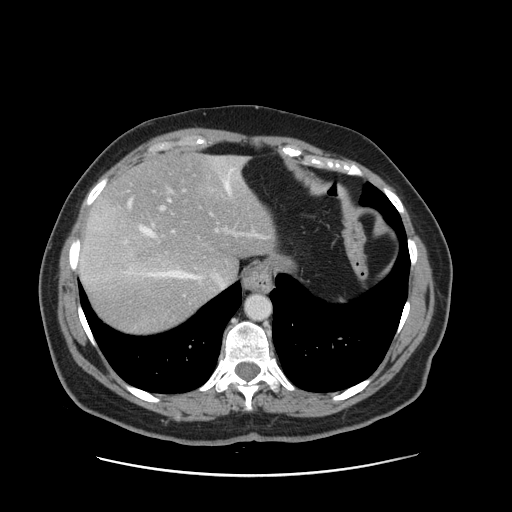
Contrast-enhanced abdominal CT, one axial slice. Slice 122 of 161 in the series (ordered by position). Intravenous contrast given. Soft-tissue window (W 400 / L 40 HU). 2.5 mm slice thickness. 512 × 512 image matrix, field of view 398 × 398 mm. Female patient, age 62 years. Case-level facts recorded for this patient, not image findings: diagnosis: colorectal cancer liver metastases, imaged before liver resection; multiple liver metastases: no; largest metastasis: 2.5 cm; disease in both lobes: no.
Structures marked on this image (manually delineated by an expert):
- hepatic veins: bounding box (x1, y1, x2, y2) in pixels: (127, 159, 244, 287)
- liver: (80, 156, 276, 335)
- planned liver remnant (the part of the liver to remain after resection): (96, 155, 275, 279)
- portal vein (with intrahepatic branches): (158, 189, 264, 238)